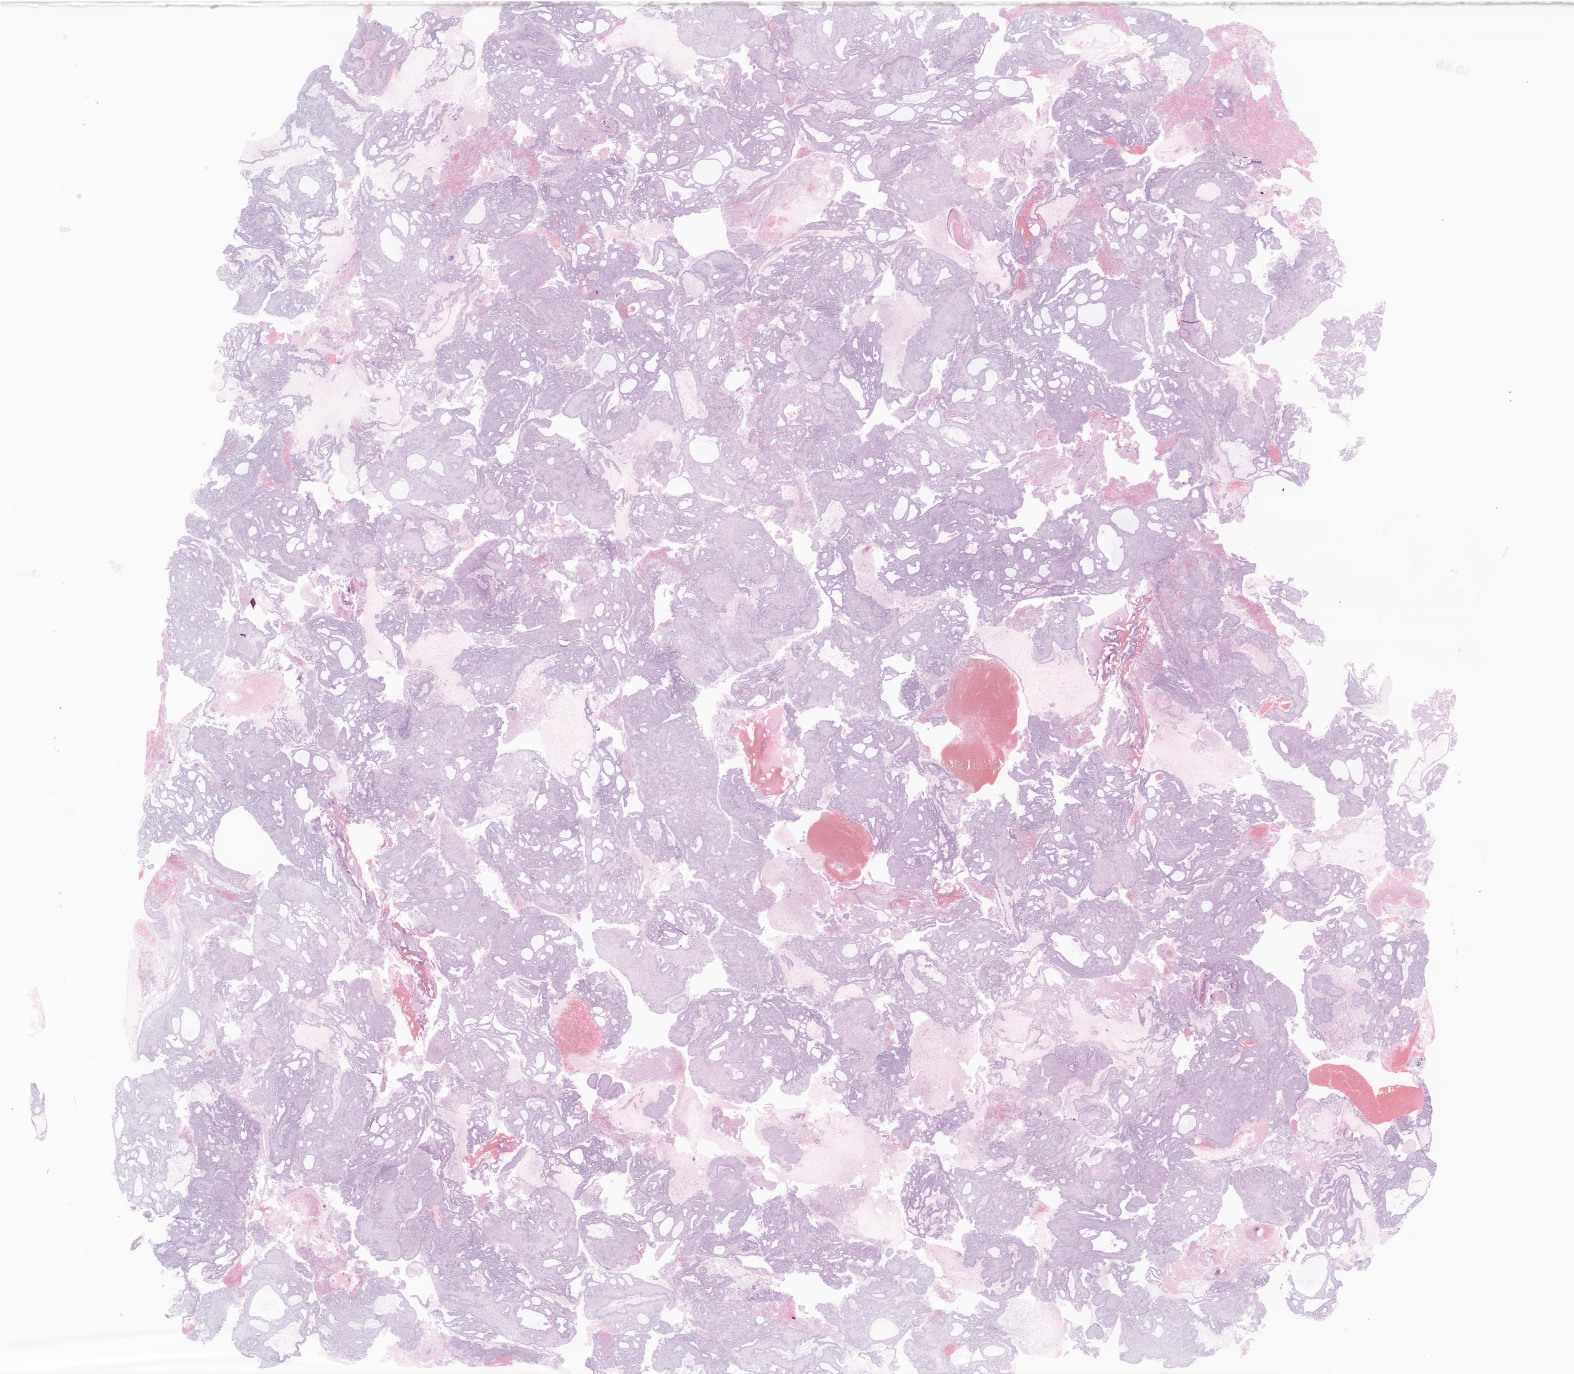
Digitized haematoxylin and eosin-stained section of tumor tissue from the brain, whole scanned area (about 26.6 x 23.2 mm) shown as a low-resolution overview. FFPE section. Patient: female, age 111 months (9 years 3 months).
• diagnosis: Craniopharyngioma, NOS